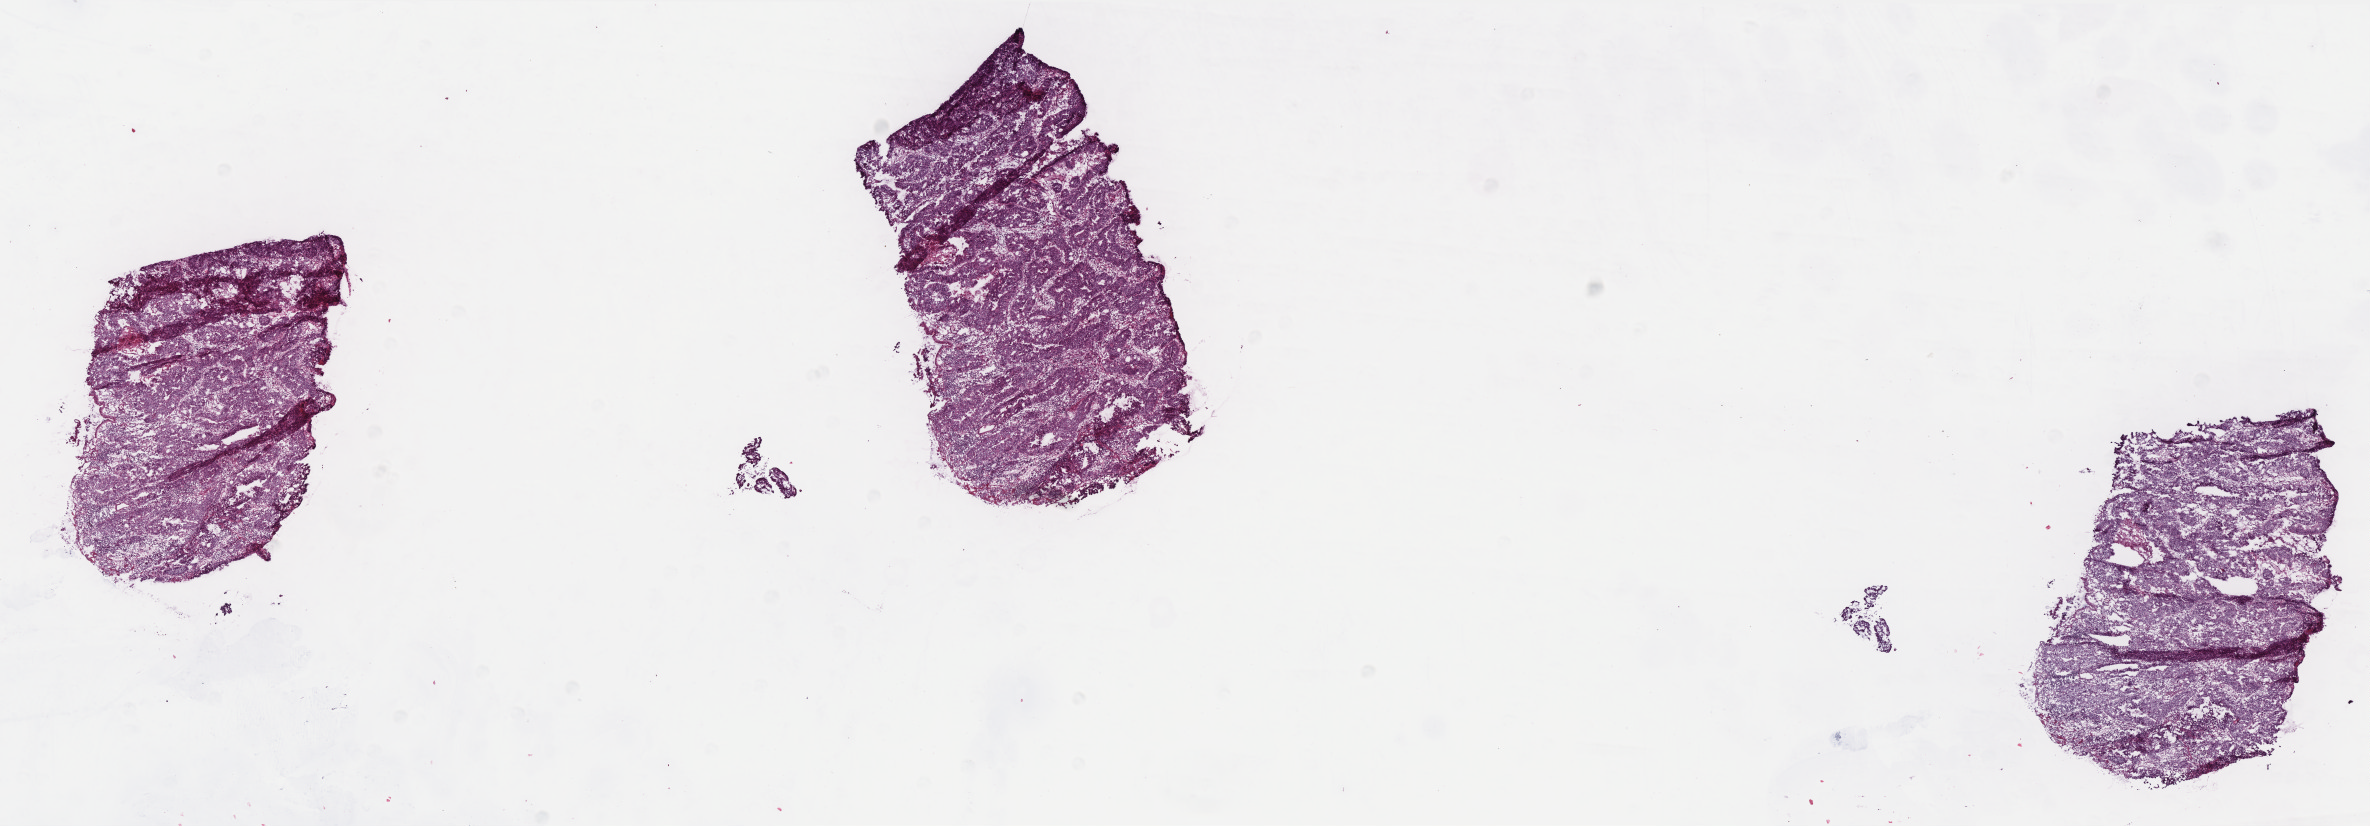
Hematoxylin and eosin (H&E) stained whole-slide image — whole scanned area (about 19.0 x 6.6 mm) shown as a low-resolution overview; frozen section; colon, primary tumour sample. Male, age 63 years at initial diagnosis. Composition of this section per pathologist review: tumour cells 97%, tumour nuclei 75%, normal cells 0%, stromal cells 2%, necrosis 1%. Infiltration values recorded for this section: lymphocyte infiltration 15%, monocyte infiltration 3%, neutrophil infiltration 2%.
- lymph nodes positive (case pathology): 0 of 22 examined
- pathologic diagnosis: Mucinous adenocarcinoma (cecum)
- AJCC pathologic stage: IIA